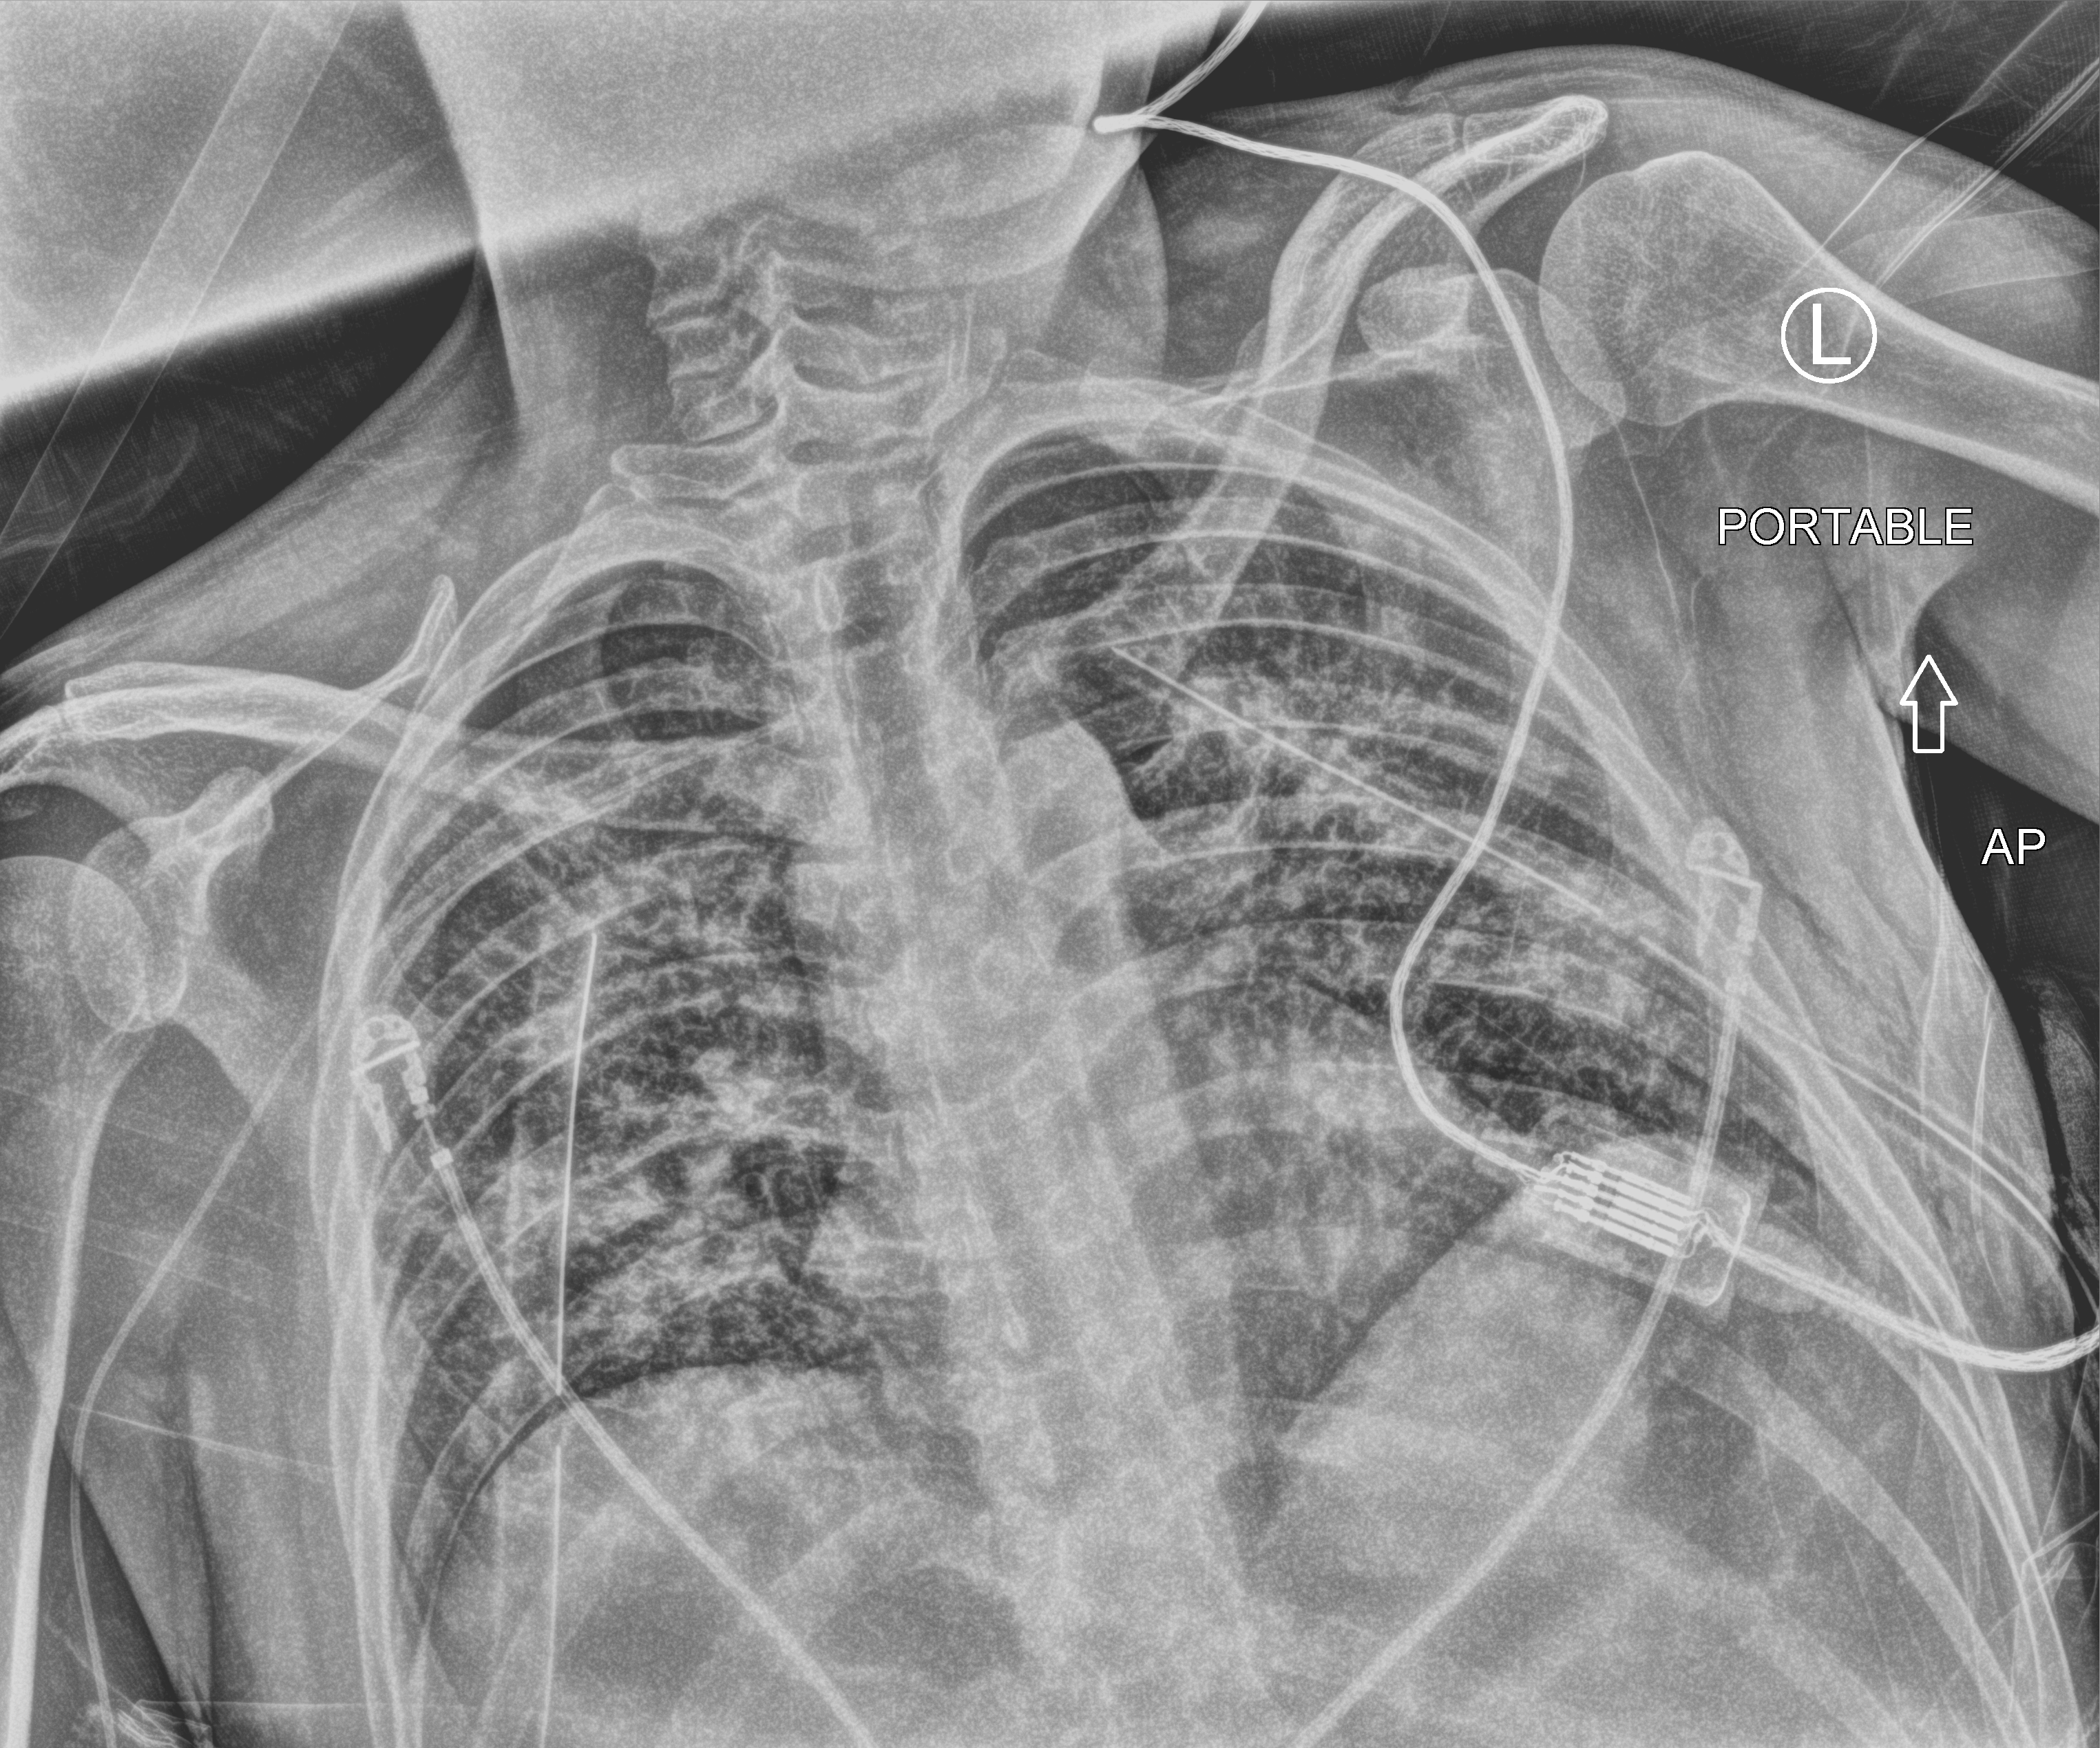
Portable chest radiograph; anteroposterior (AP) projection. Male patient hospitalised with COVID-19, age 18–59 years.
Hospital-stay facts (about this admission, not read from this image; timing relative to this image not recorded):
- other chronic lung disease (admission record): no
- admitted to intensive care during this hospital stay: yes
- mechanically ventilated during this hospital stay: yes